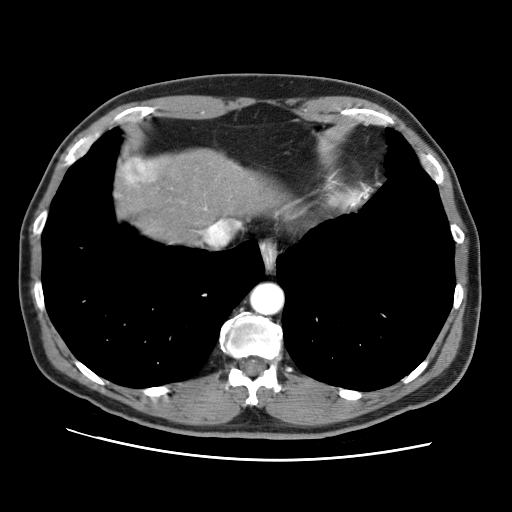
Contrast-enhanced abdominal CT (liver protocol), one axial slice. Slice 63 of 71 in the series (ordered by position). Reconstruction kernel STANDARD. Soft-tissue window (W 400 / L 40 HU). 2.5 mm slice thickness. 512 × 512 image matrix. Case-level facts recorded for this patient, not image findings: diagnosis: hepatocellular carcinoma (patient treated with transarterial chemoembolisation; whether this scan precedes or follows treatment is not stated here); TNM stage (as recorded): Stage-II; Child-Pugh class: A; tumour differentiation: well differentiated; tumour size: 4.6 cm.
Structures marked on this image (semi-automatic segmentation, software-assisted and operator-edited):
- liver parenchyma outside the tumour (the mass and vessels are separate outlines, so this box may not span the whole liver): bounding box [x1, y1, x2, y2] px = [116, 150, 278, 240]
- mass: [122, 158, 150, 184]
- liver vessels: [143, 164, 152, 168]